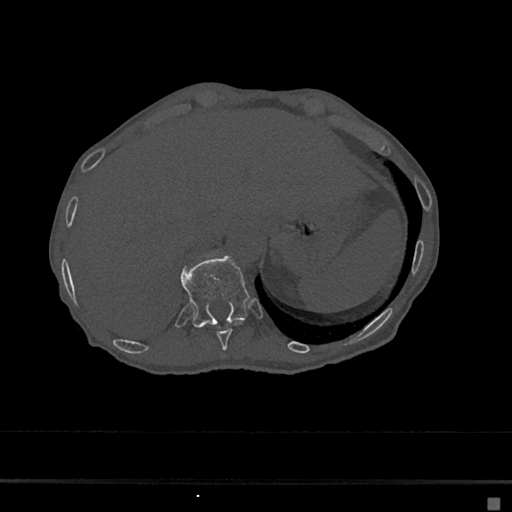
CT including the spine, one axial slice; position 189 of 797 along the scan axis; reconstruction kernel Br40s/3; 120 kVp; bone window (W 1800 / L 400 HU); 512 × 512 image matrix, field of view 360 × 360 mm. Patient: female, 68 years. From the clinical record (not read from this slice): primary cancer: renal.
Annotated regions visible in this slice (semi-automatic segmentation, software-assisted and operator-edited):
- T10 vertebra: bounding box <216,321,243,350> (left, top, right, bottom; pixels)
- T11 vertebra: <181,256,250,327>